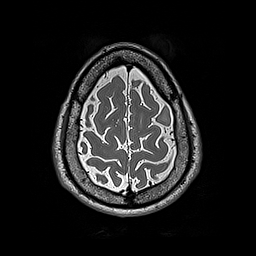
Brain MRI from a brain-tumour surgery series, one axial slice; slice 53 of 192 in the series (ordered by position); 1 mm slice thickness; 256 × 256 image matrix, field of view 250 × 250 mm. From the clinical record (not read from this slice): histopathology: Astrocytoma; WHO grade: 2; IDH mutation: yes; tumour location: Left Frontal.
Outlined on this slice (manually delineated by an expert):
- tumour: bounding box [x1, y1, x2, y2] px = [158, 108, 168, 124]